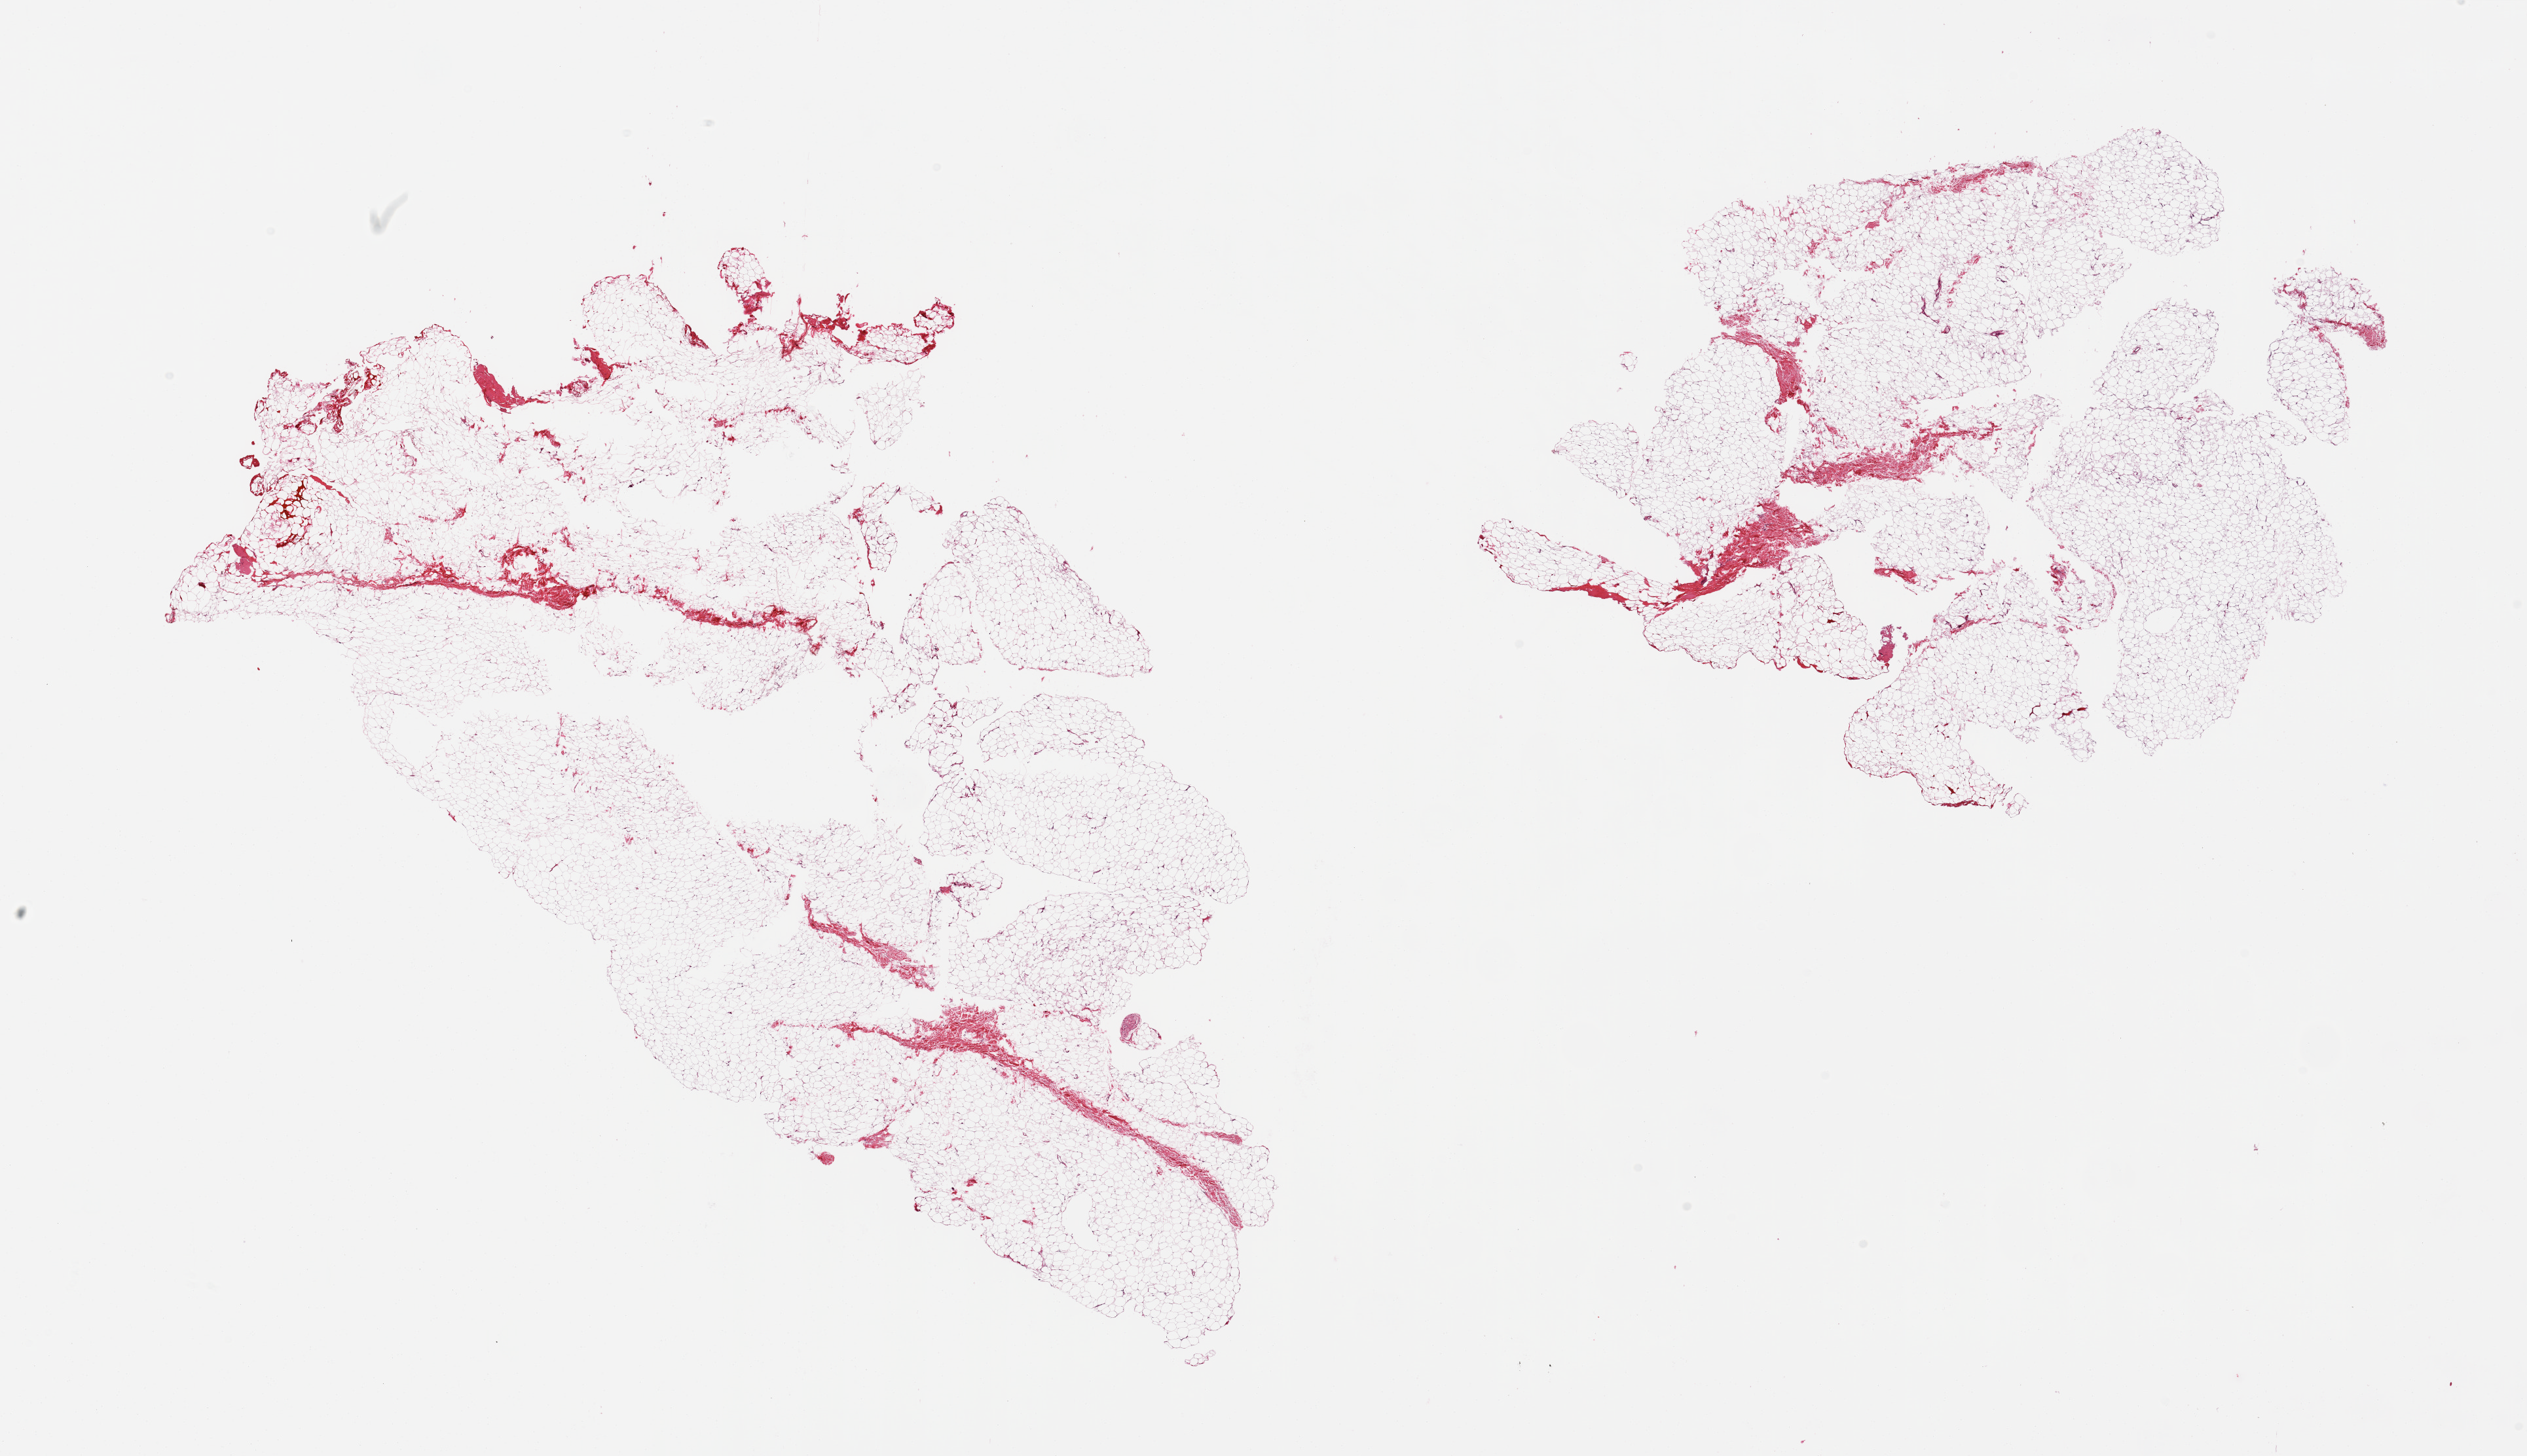
Hematoxylin and eosin (H&E) whole-slide image — shown as a low-resolution overview of the whole scanned area (about 30.5 x 17.6 mm, slide scanned at 20x); PAXgene-fixed paraffin-embedded (PFPE) section; section of adipose tissue (target tissue); tissue donor sample. Male donor.
Review note (as recorded): 2 pieces; <2% fibrous content.